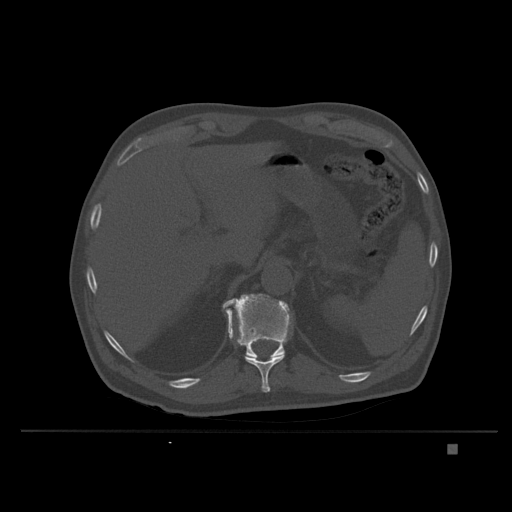
CT including the spine, one axial slice. Bone window (W 1800 / L 400 HU). 1.5 mm slice thickness. 512 × 512 image matrix, field of view 434 × 434 mm. Male patient, age 73 years. Case-level facts recorded for this patient, not image findings: primary cancer: skin.
Outlined on this slice (semi-automatically segmented with operator editing):
- T11 vertebra: bounding box [x1, y1, x2, y2] px = [227, 311, 285, 393]
- T12 vertebra: [222, 293, 293, 358]